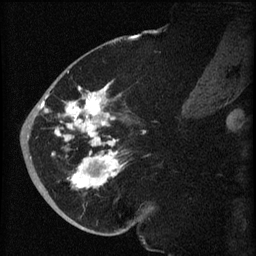
Breast MRI (dynamic contrast-enhanced), one sagittal slice. Slice 28 of 60 in the series (ordered by position). Dynamic contrast-enhanced series, image 2 of 3 at this slice position (ordered by acquisition). 1.5 T. TE 4.2 ms, TR 8.2 ms. 2 mm slice thickness. 256 × 256 image matrix. Patient: female, 71 years.
Outlined on this slice (semi-automatically segmented with operator editing):
- analysis volume of interest (the breast-tissue region the enhancement analysis was run in; not a lesion): bounding box (x1, y1, x2, y2) in pixels: (40, 72, 140, 196)
- tumour enhancement mask (voxels above the 70 % enhancement threshold inside the analysis volume of interest): (40, 82, 122, 189)